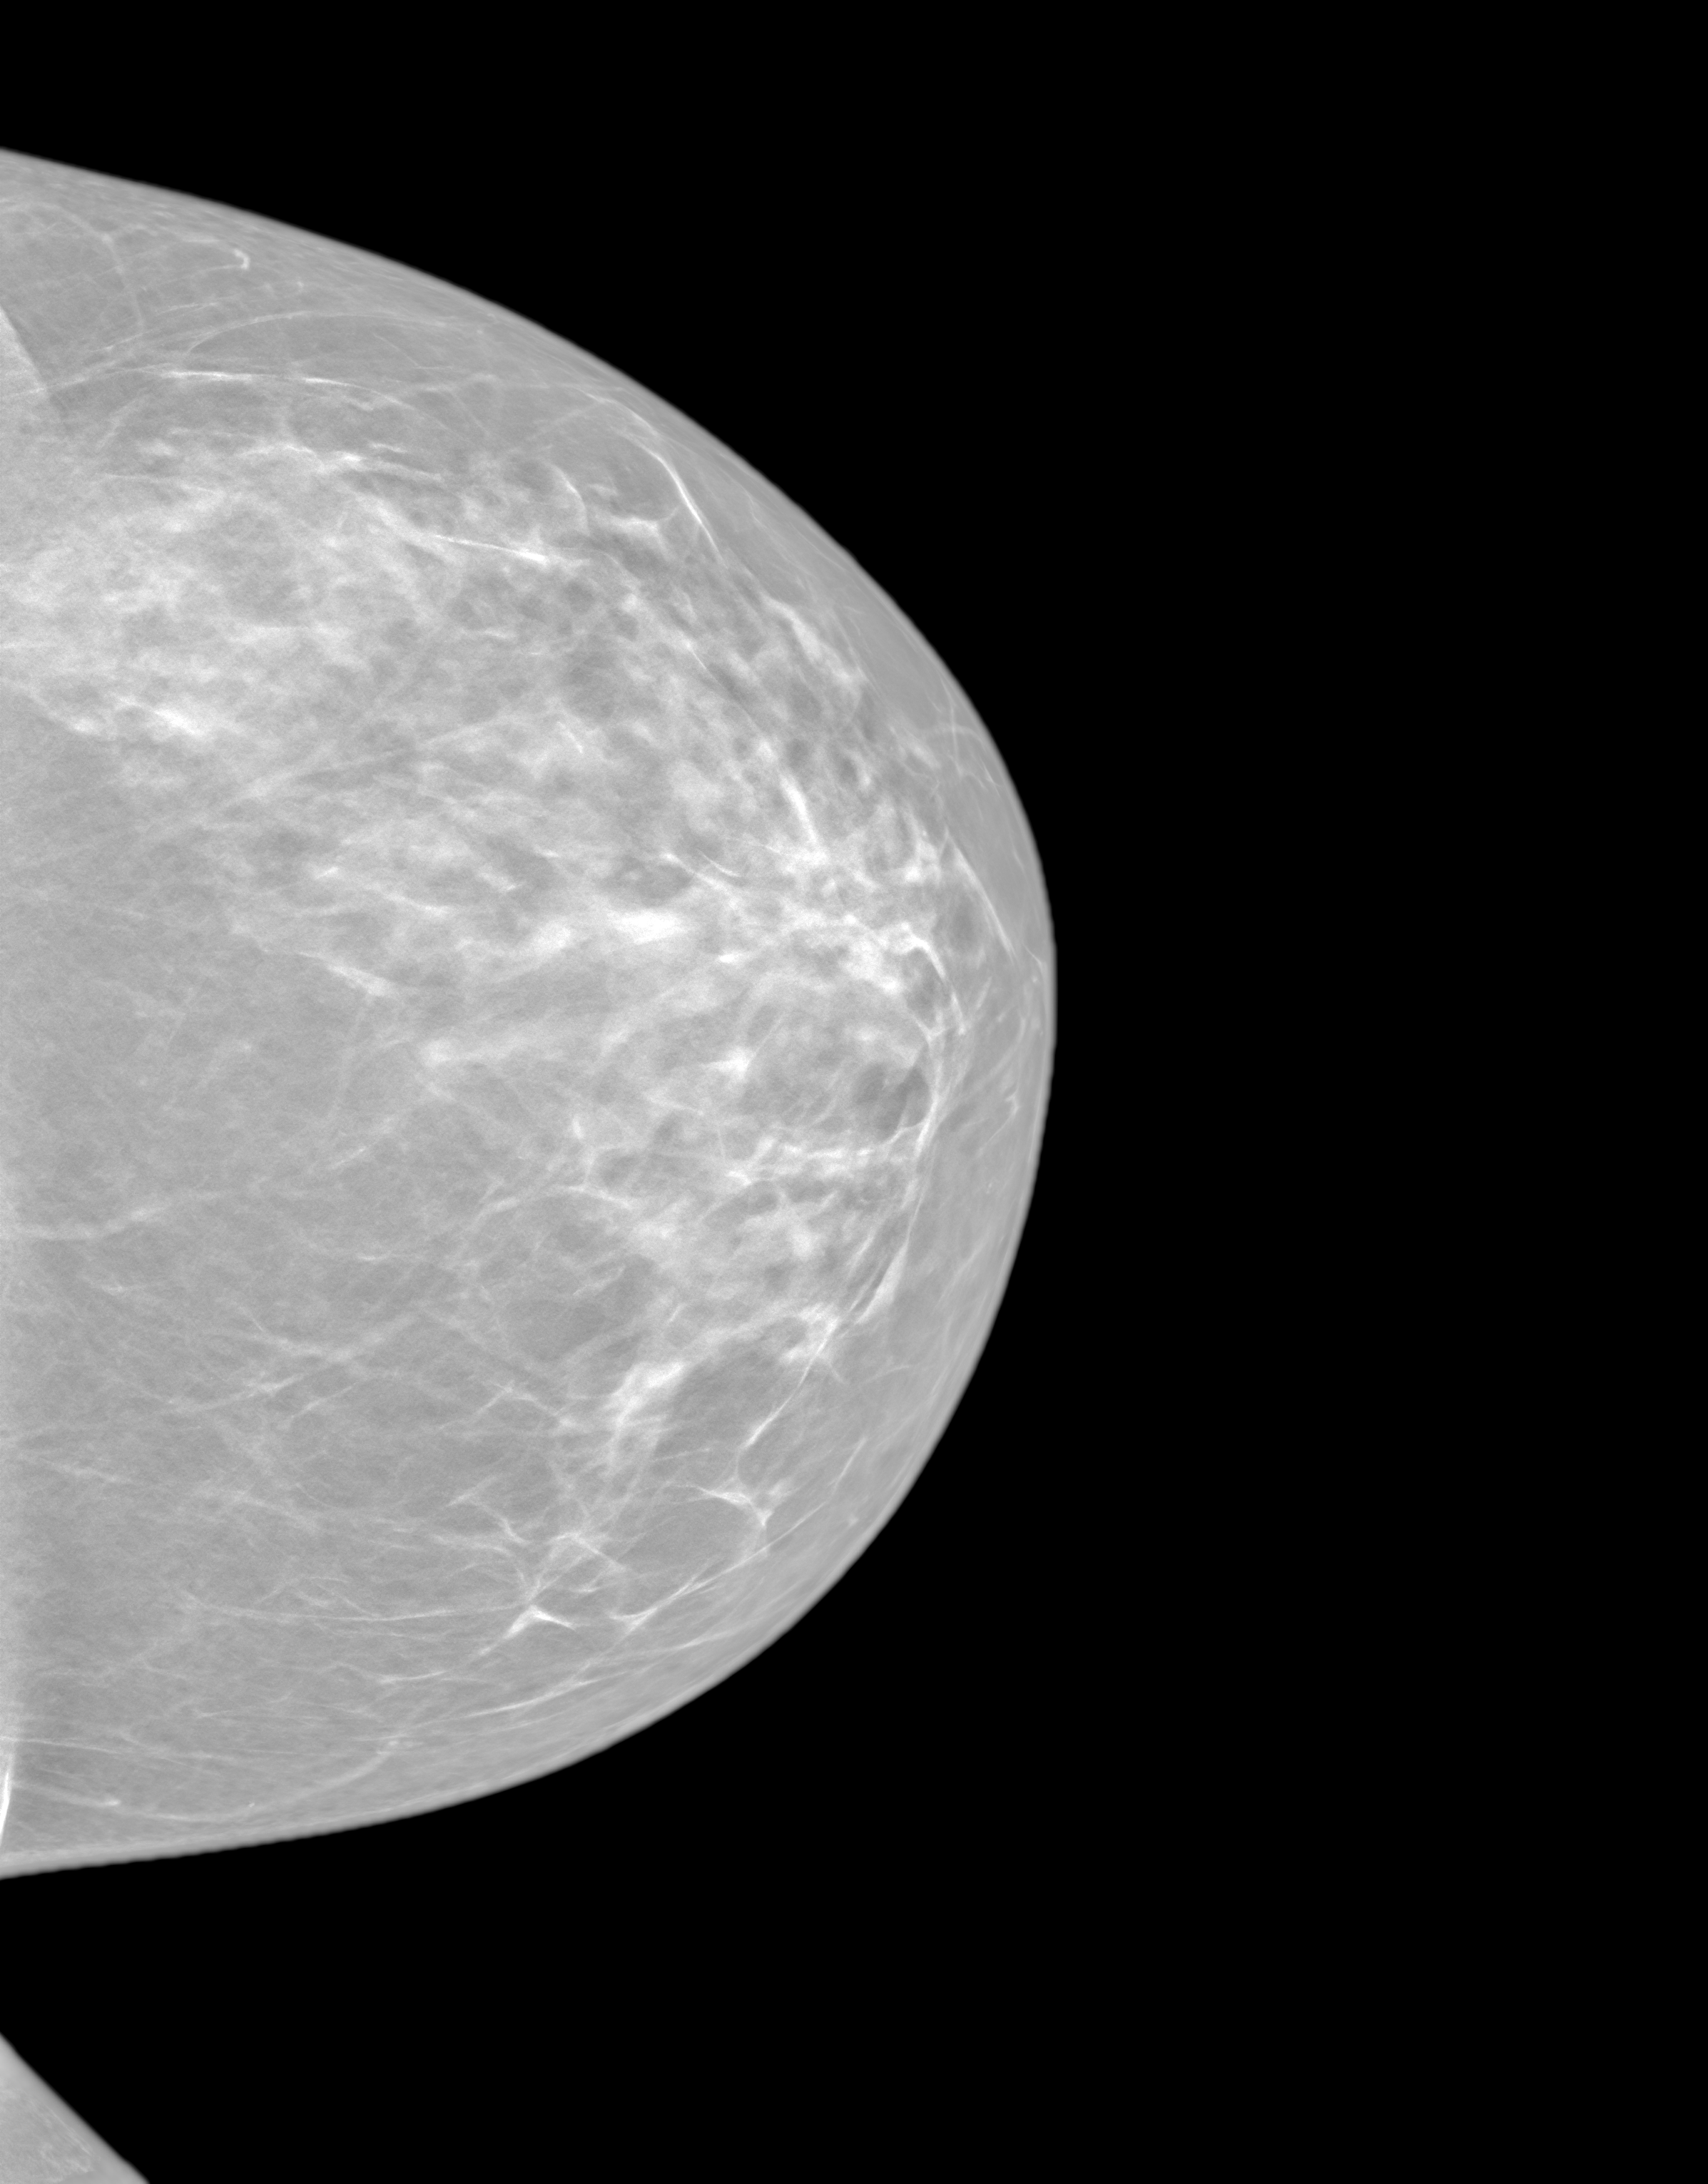
Synthesized 2-D mammogram reconstructed from digital breast tomosynthesis, left breast, cranio-caudal projection, screening examination, system: SenoIris_1SP1.1(421). Female patient, age 42 years.
Breast density at the screening exam (both breasts): heterogeneously dense (BI-RADS density category c). Final BI-RADS assessment for this screening round (tomosynthesis exam, both breasts): category 1. Recall: no recall after this screen.